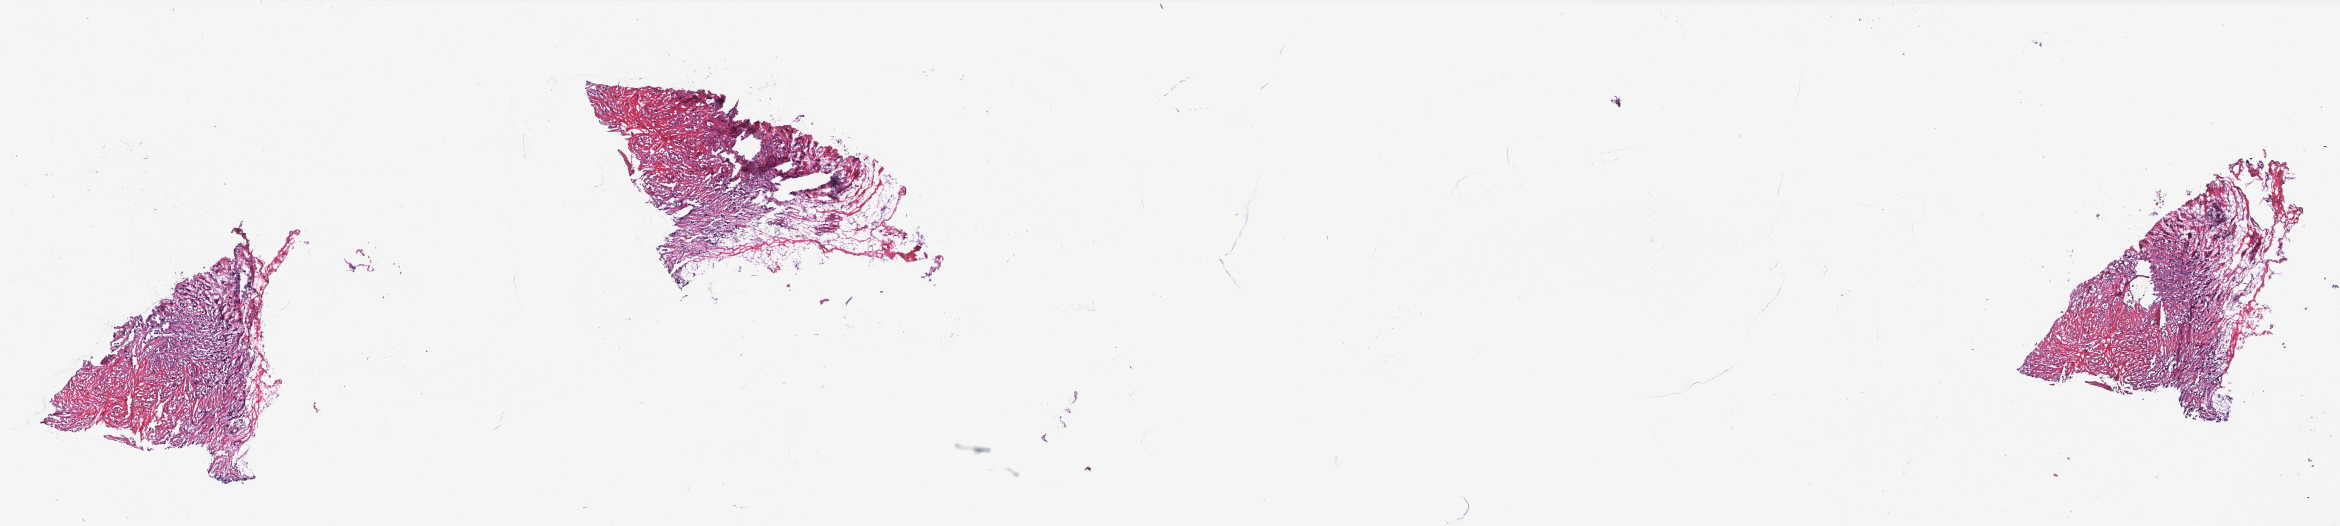
H&E whole-slide image — shown as a low-resolution overview of the whole scanned area (about 37.5 x 8.4 mm, from a 40x scan). Frozen section from the top of the tissue portion. Breast, primary tumour sample. Patient: female, age at initial diagnosis 49 years. Slide review estimates, as recorded: tumour cells 90%, tumour nuclei 80%, normal cells 0%, stromal cells 10%, necrosis 0%. Inflammatory infiltration, as recorded: lymphocyte infiltration 0%, monocyte infiltration 0%, neutrophil infiltration 0%.
* lymph nodes positive (case pathology): 14 of 23 examined
* TNM: T2 N3a MX
* diagnosis: Infiltrating duct carcinoma, NOS
* AJCC pathologic stage: IIIC